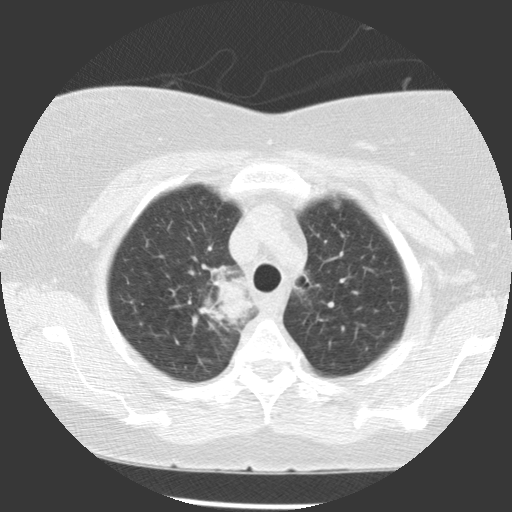
Chest CT (low-dose screening protocol), one axial image; baseline annual screen; lung window (W 1500 / L -600 HU); slice 92 of 116 in the series; 512 × 512 image matrix. Female, age 63 years at enrolment. Former smoker at enrolment.
Expert reader's lesion annotation, bounding box (x1, y1, x2, y2) in pixels: (201, 267, 259, 329). Reader record for this screening exam (exam-level; its link to the box is not recorded): non-calcified nodule or mass ≥4 mm, right upper lobe, 39 × 36 mm, spiculated (stellate) margins, soft tissue attenuation. Official screen result: positive, change unspecified: nodule(s) >= 4 mm or enlarging nodule(s), mass(es), or other non-specific abnormalities suspicious for lung cancer. Later outcome: lung cancer diagnosed 72 days after this screen — non-small cell carcinoma, right upper lobe, carina, right main stem bronchus, poorly differentiated (G3), stage IIIA (AJCC 6th edition), 66 mm at pathology.